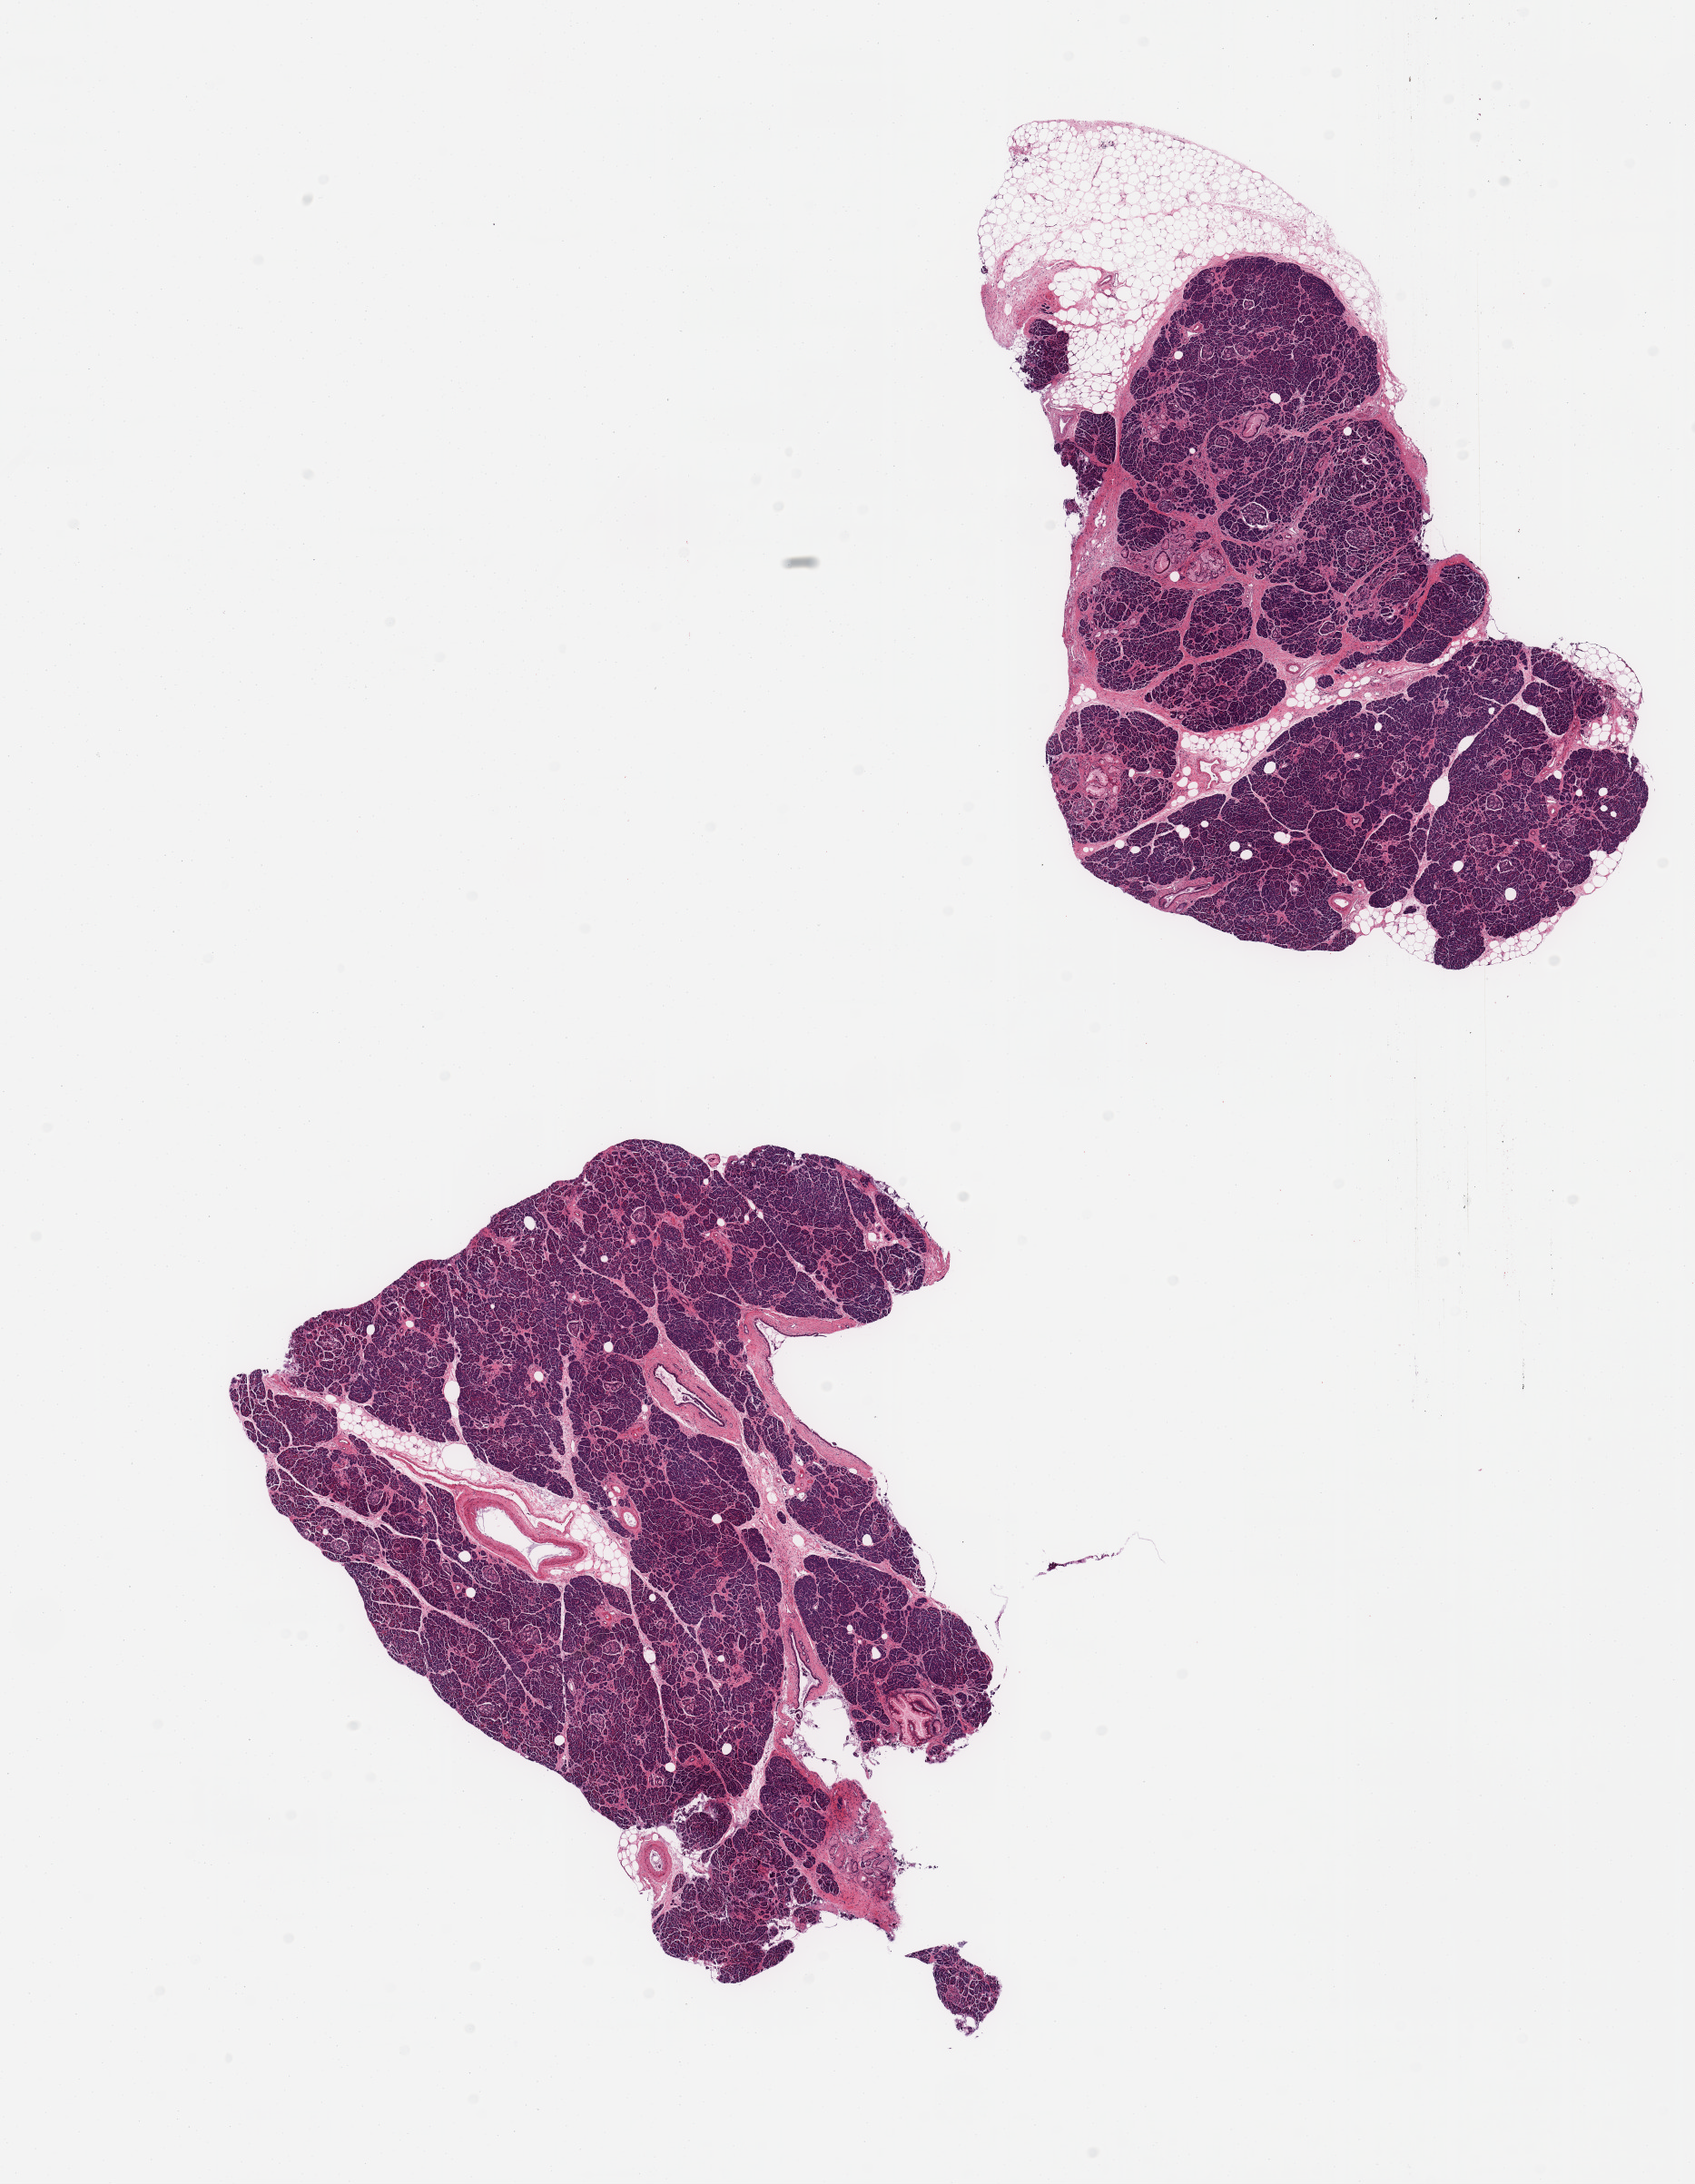
Whole-slide image, haematoxylin and eosin stain, a low-resolution overview of the entire scanned area, about 14.8 x 19.0 mm. PAXgene-fixed paraffin-embedded (PFPE) section. Section of pancreas (target tissue). Tissue donor sample. Donor: female.
Pathologist's review note for this sample: 2 pieces; mild autolysis of parenchyma and septal fat; mild interstitial fibrosis; preserved Langerhans islets; scattered pancreatic ducts lined by mucinous rich cytoplasm cells/Pan1N.